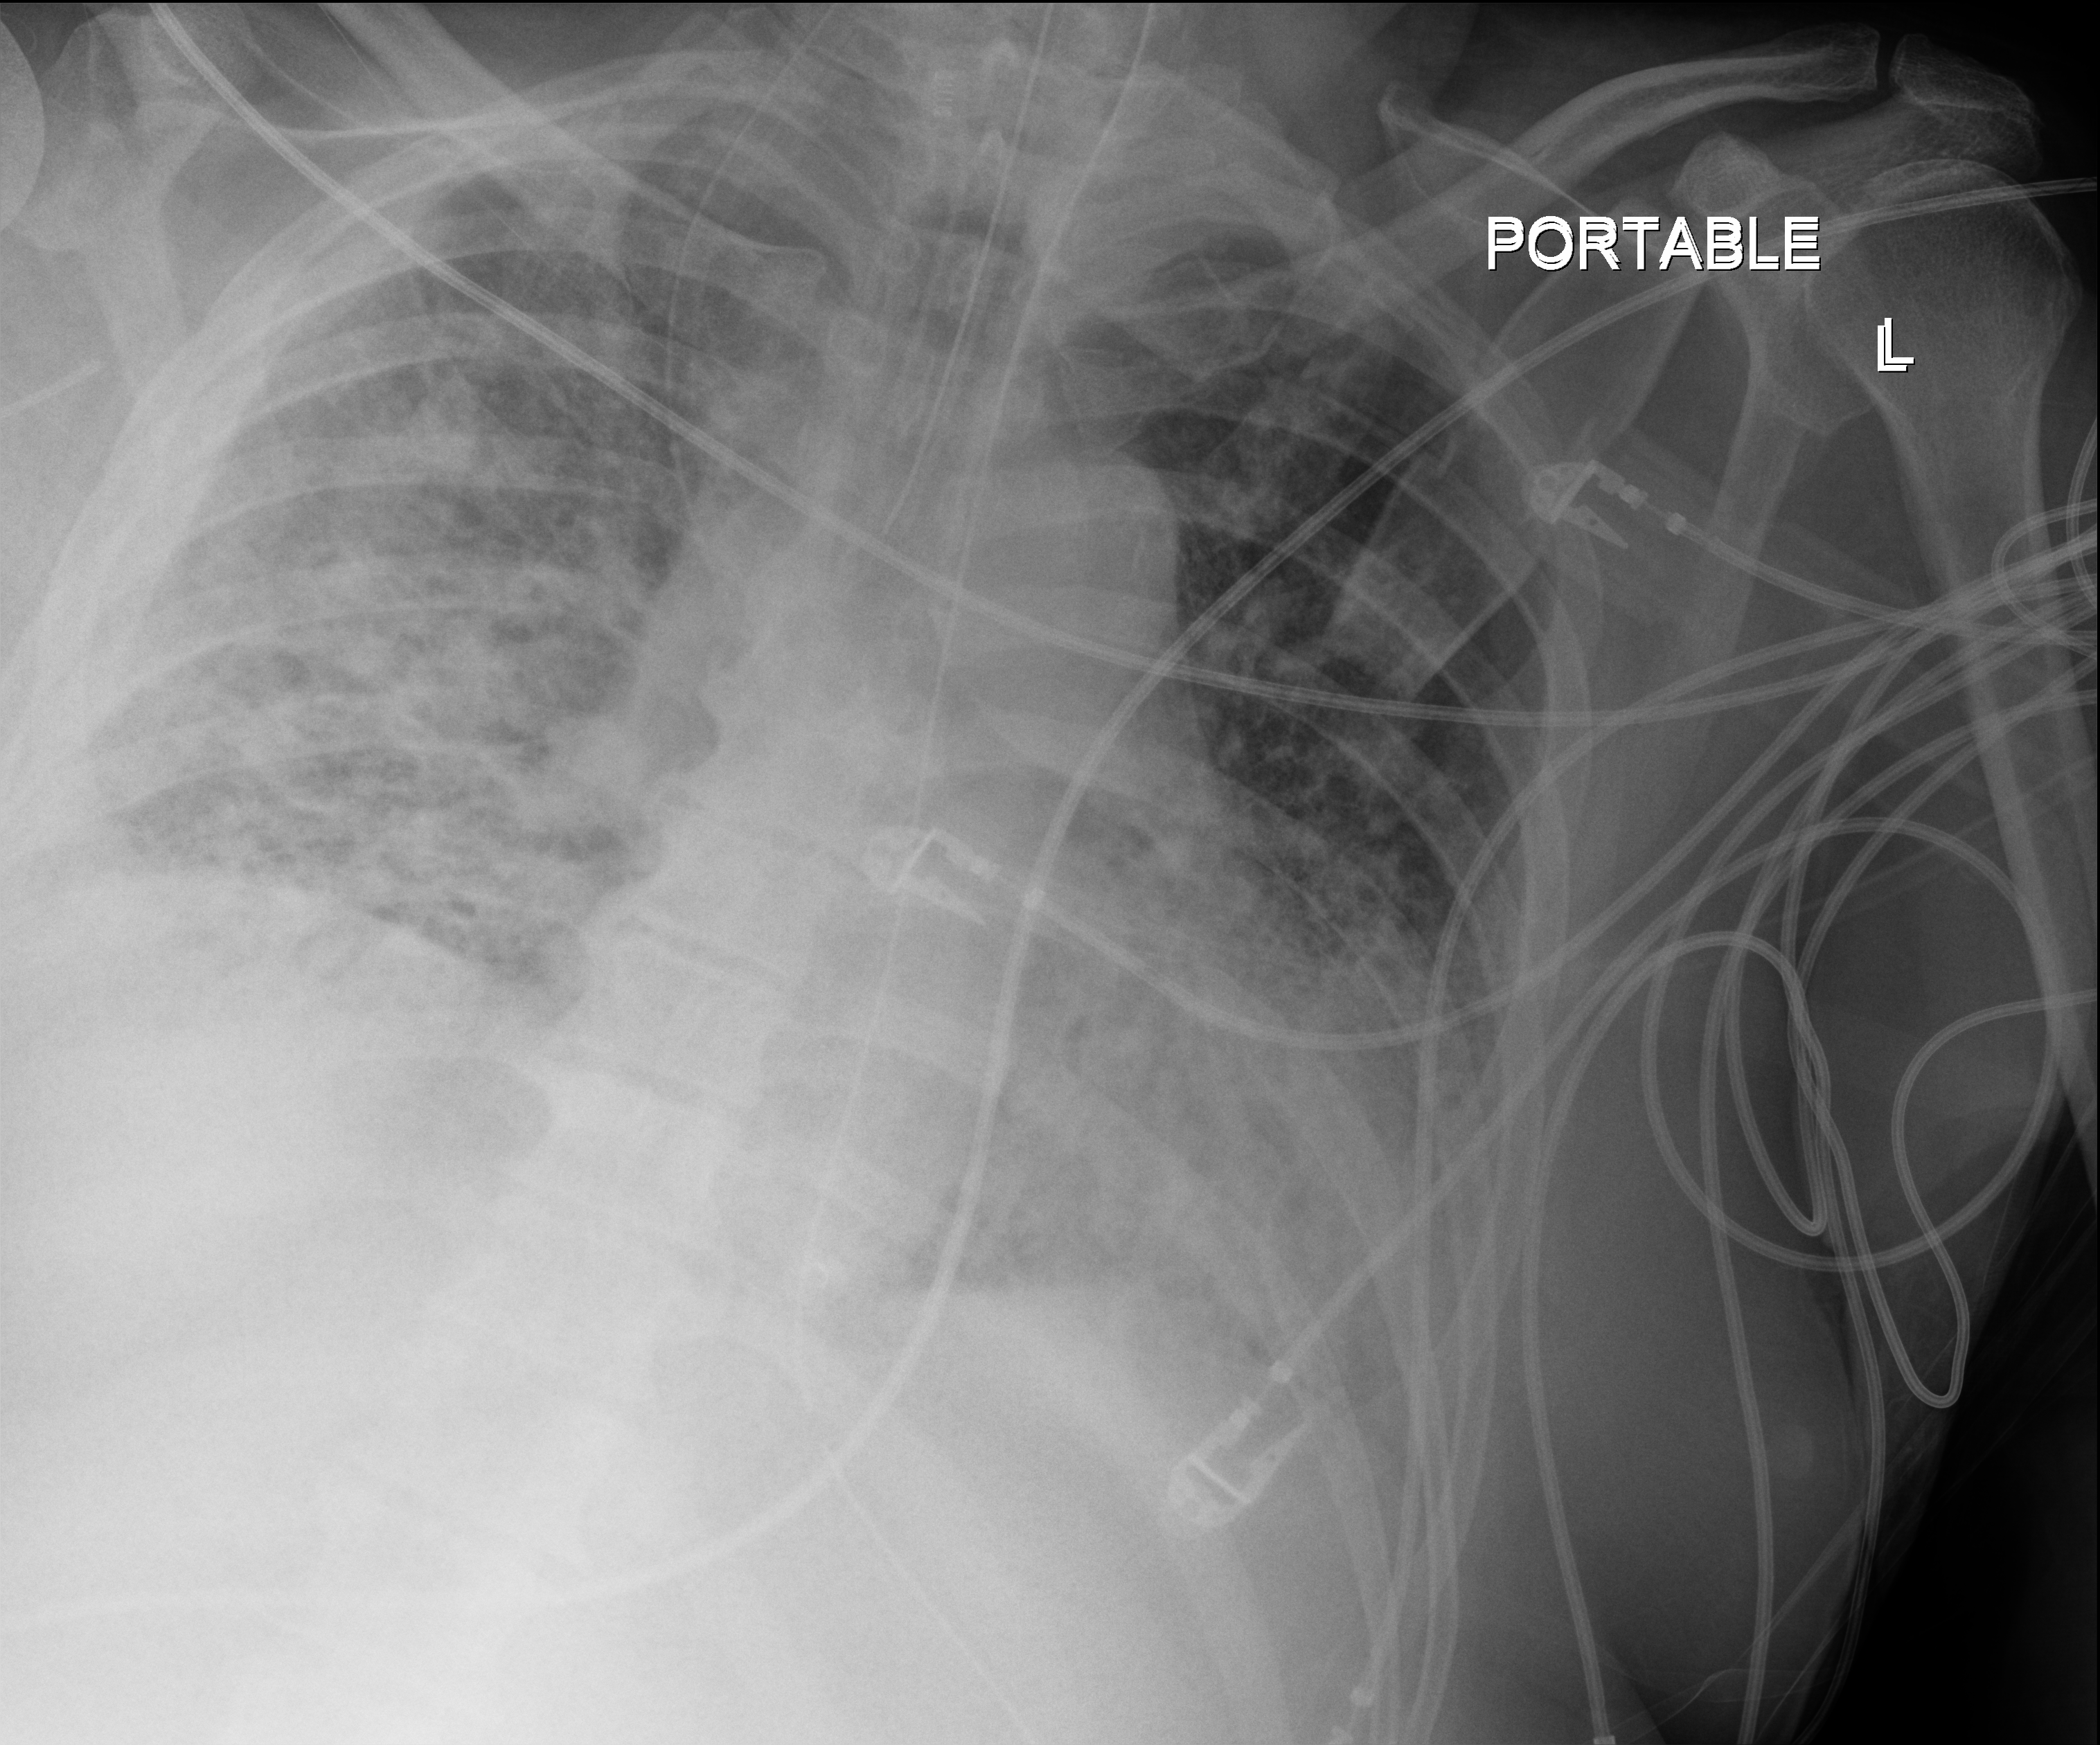
Chest X-ray (portable); anteroposterior (AP) projection. Patient hospitalised with COVID-19; male, aged 60–74 years.
Admission-level facts for this patient (not findings on this image; timing relative to this image not recorded): length of hospital stay: 40 days.